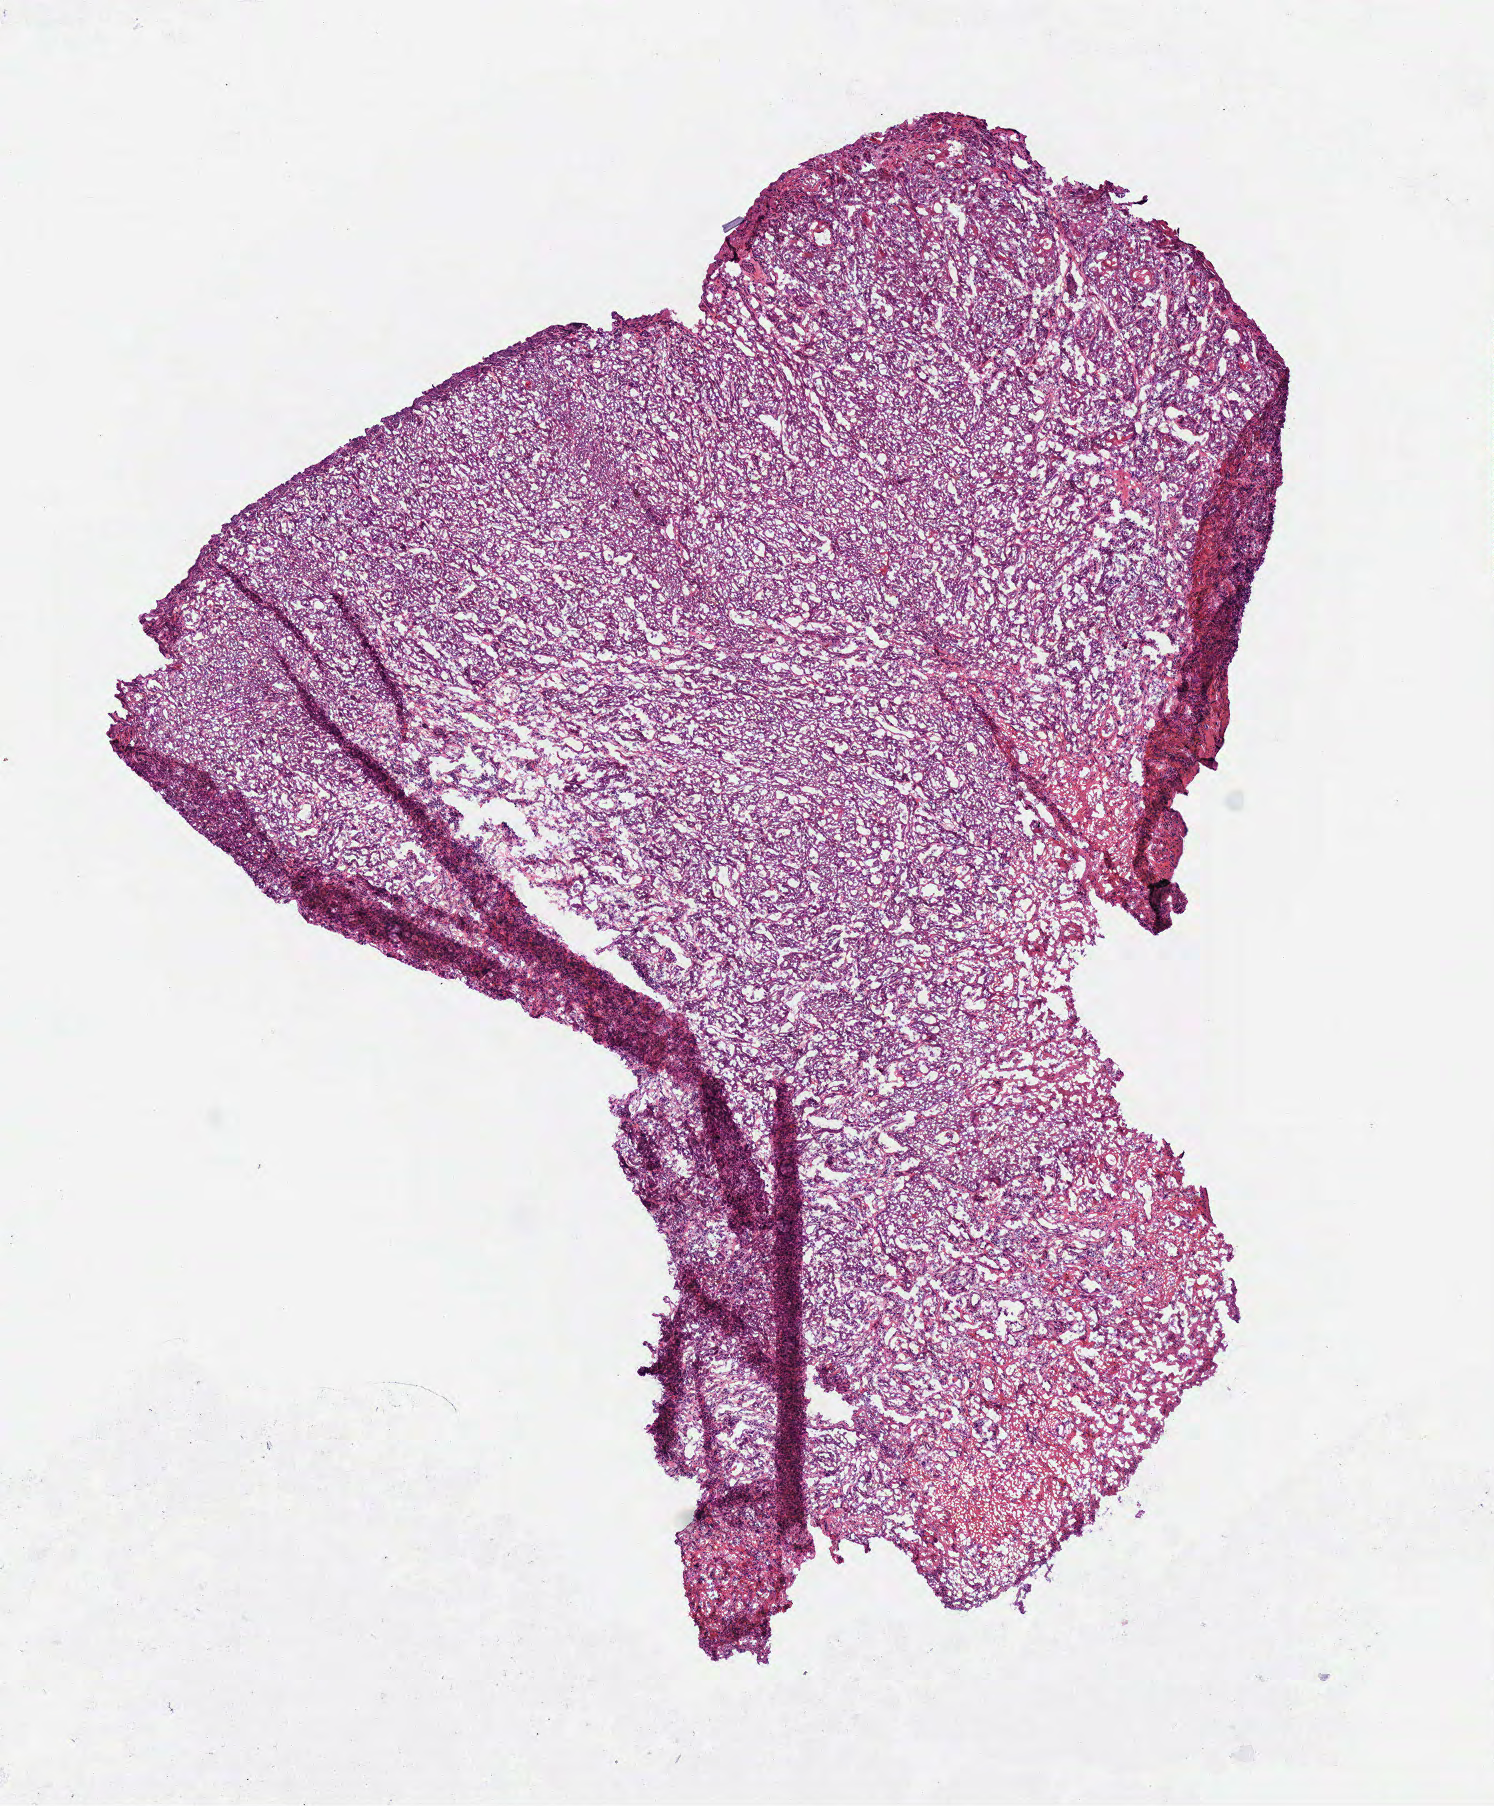
Digitized H&E tissue section (whole slide), low-resolution overview of the scanned area, about 5.9 x 7.1 mm (acquisition: 40x scan), frozen section from the top of the tissue portion, sample: primary tumour, head and neck. Patient: male, age at initial diagnosis 74 years. Histologic grade: G2 (moderately differentiated). Composition of this section per pathologist review: tumour cells 90%, tumour nuclei 65%, normal cells 0%, stromal cells 10%, necrosis 0%.
• pathologic diagnosis: Squamous cell carcinoma, NOS (larynx, NOS)
• AJCC pathologic stage: IVA (7th edition)